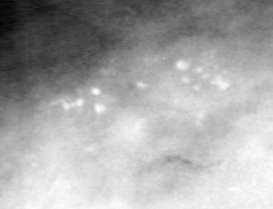
Cropped region of a digitized screen-film mammogram centred on a radiologist-marked abnormality; left breast; CC view.
Calcifications, morphology pleomorphic, distribution clustered; BI-RADS assessment category 4; pathology result (as recorded, not read from the image): malignant.